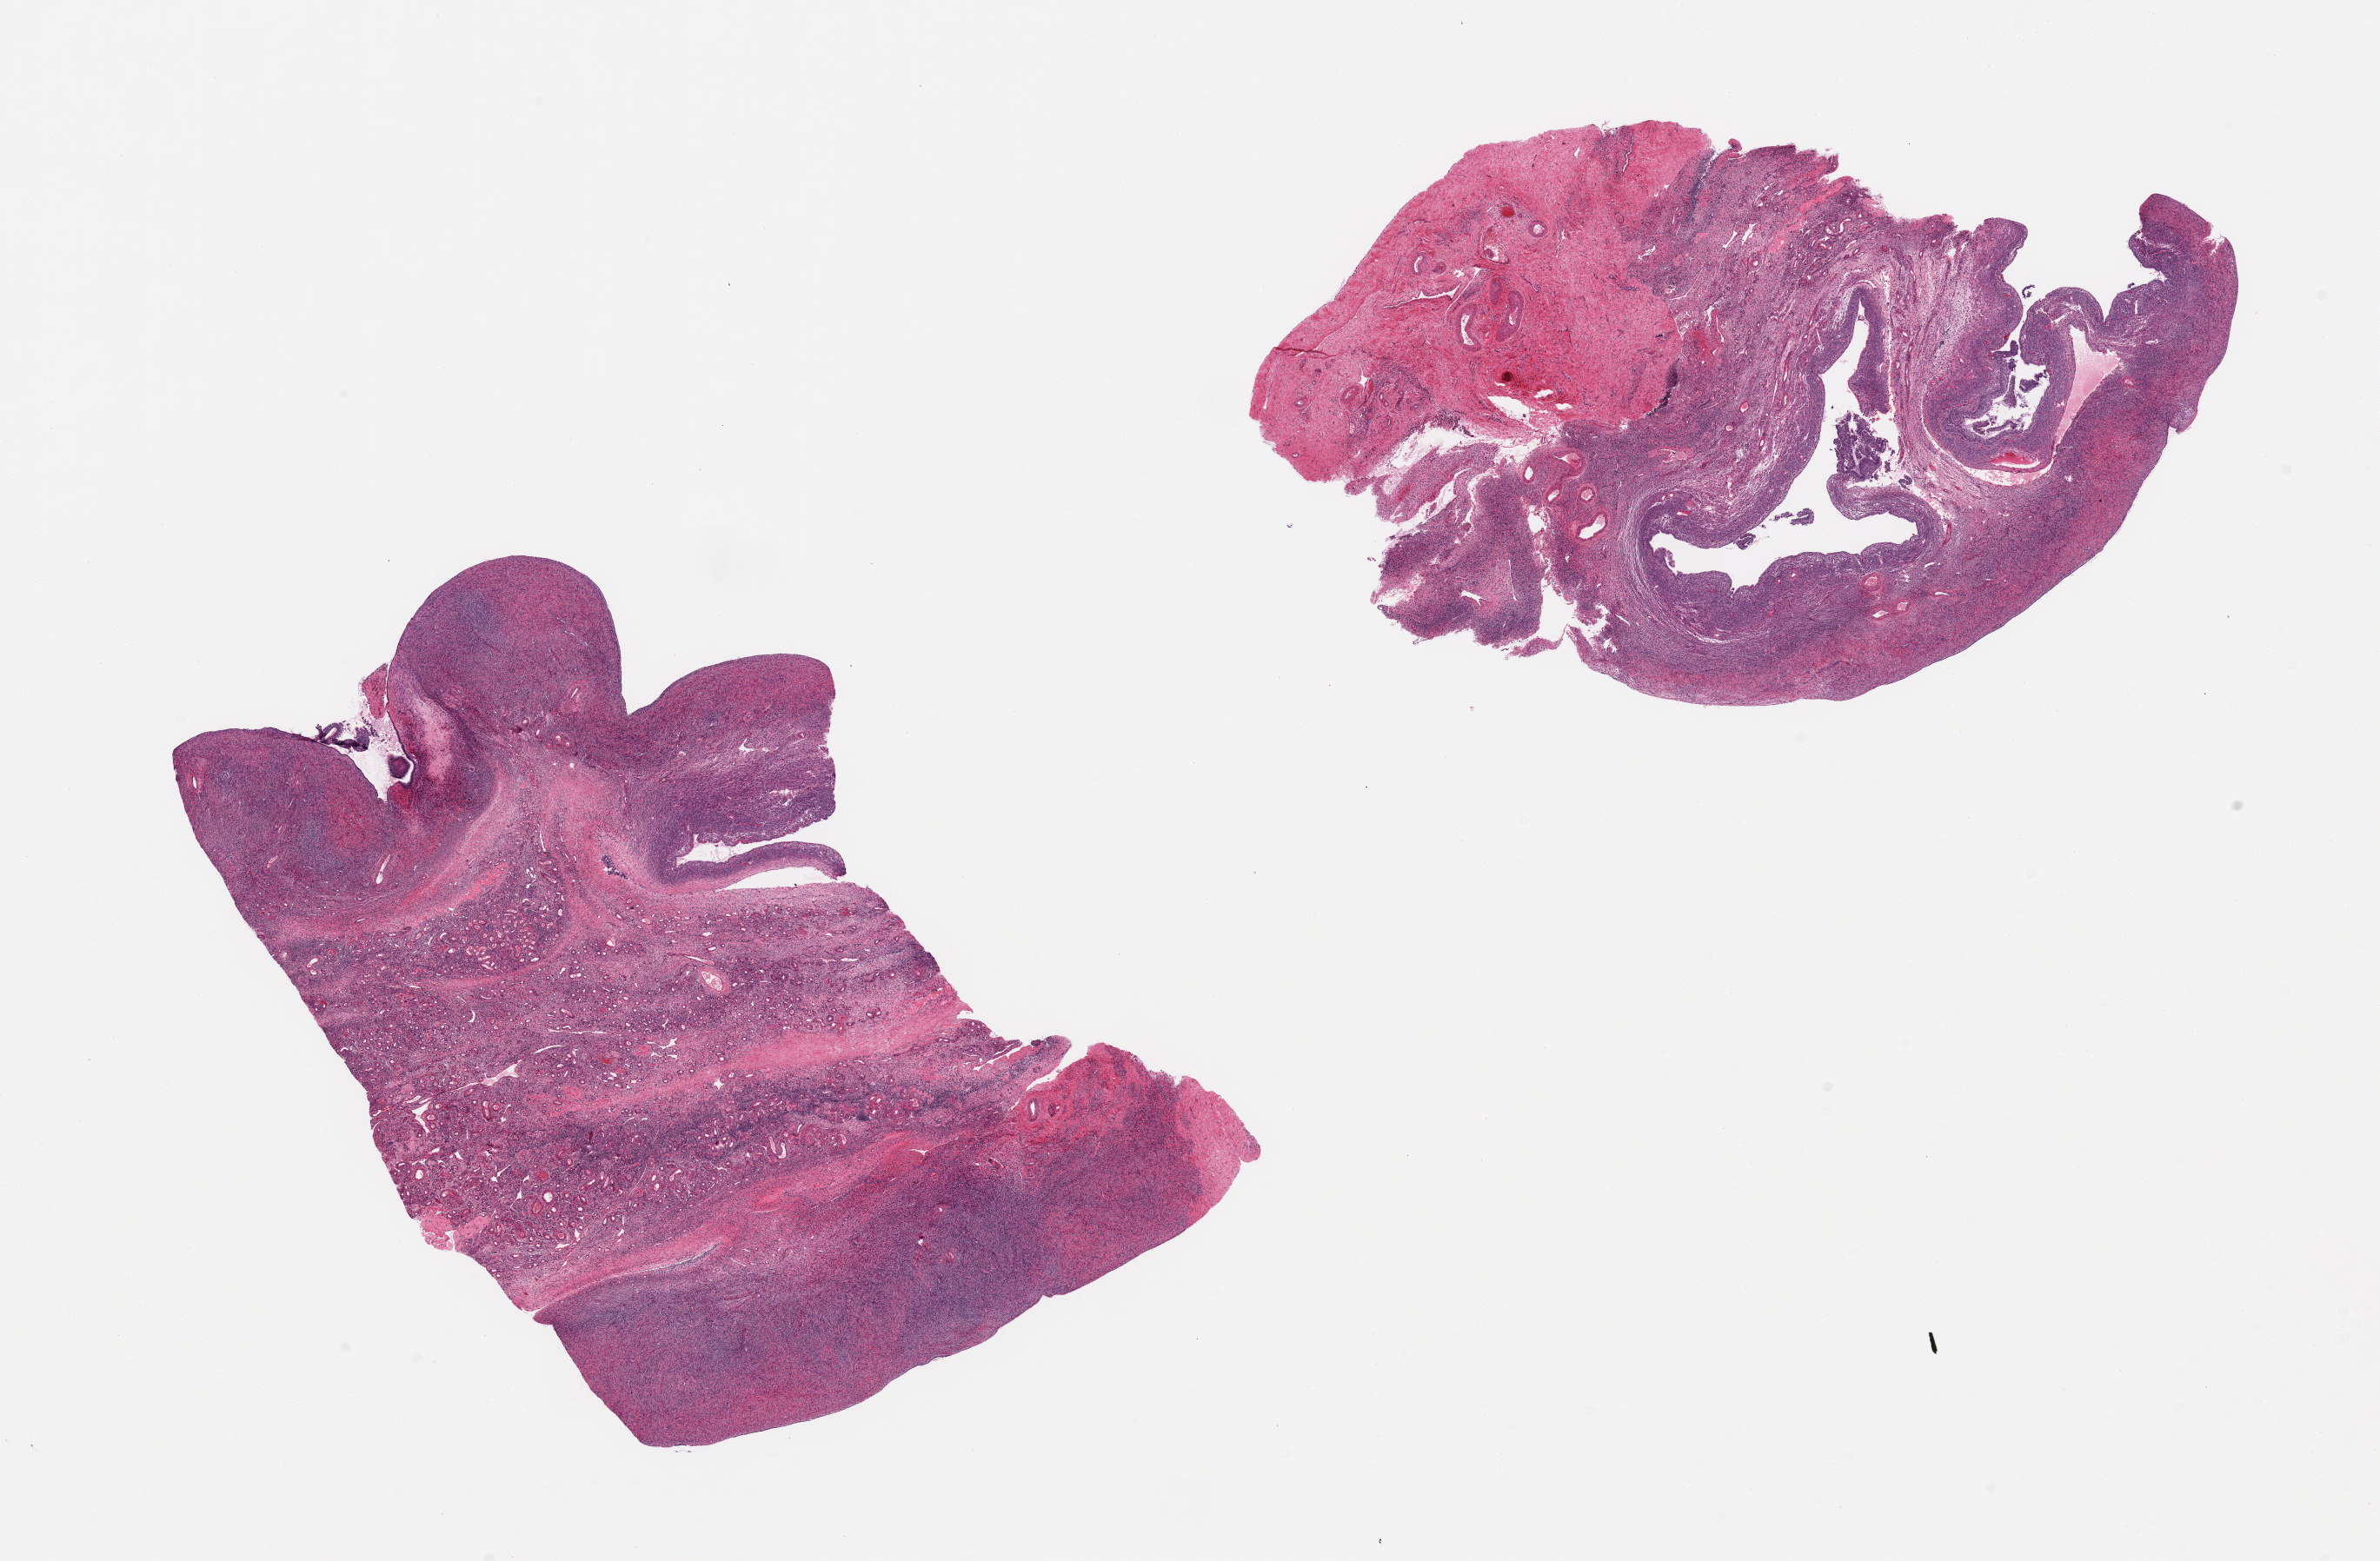
Whole-slide image, haematoxylin and eosin stain, brightfield, low-resolution overview of the scanned area, about 21.7 x 14.2 mm (acquisition: 20x scan); PAXgene-fixed, paraffin-embedded tissue; target tissue: ovary; tissue donor sample.
Review note (as recorded): 2 pieces; several large follicular cysts.